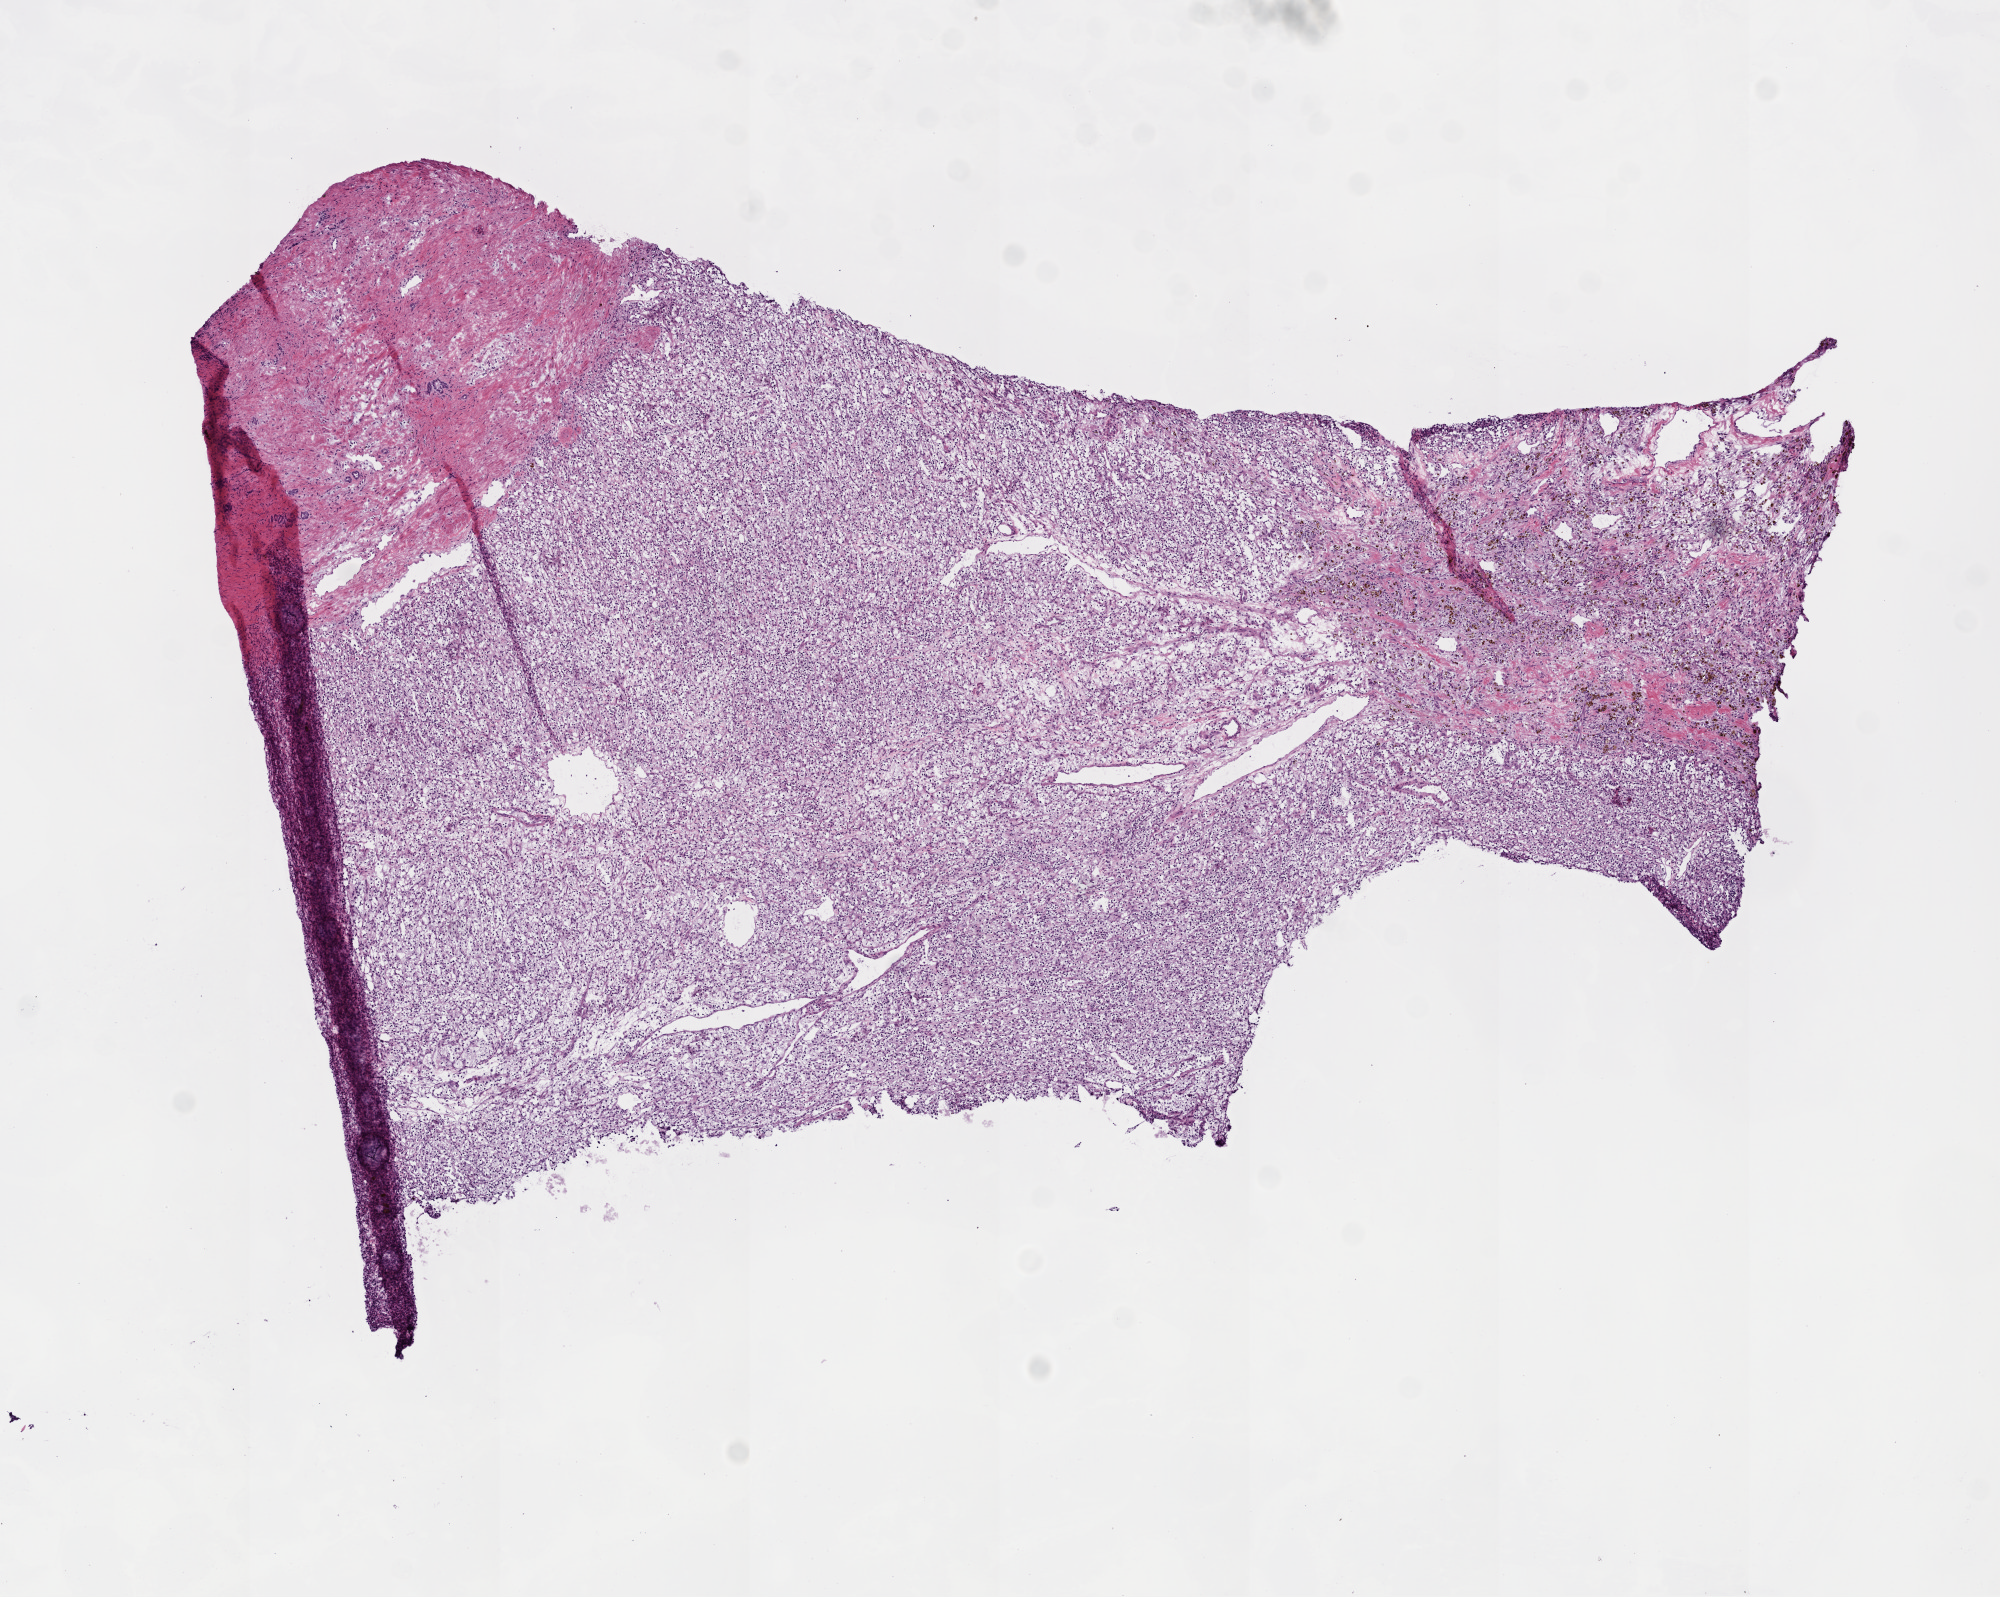
H&E-stained whole-slide image — whole scanned area (about 8.0 x 6.4 mm) shown as a low-resolution overview. Frozen section from the top of the tissue portion. Kidney, primary tumour sample. Male patient; age at initial diagnosis 52 years. Histologic grade: G2 (moderately differentiated). Slide review estimates, as recorded: tumour cells 80%, tumour nuclei 85%, normal cells 10%, stromal cells 10%, necrosis 0%. Inflammatory infiltration, as recorded: lymphocyte infiltration 3%, monocyte infiltration 3%, neutrophil infiltration 0%.
Laterality: left. Histologic diagnosis: Clear cell adenocarcinoma, NOS. TNM: T1a NX M0. AJCC pathologic stage: I.